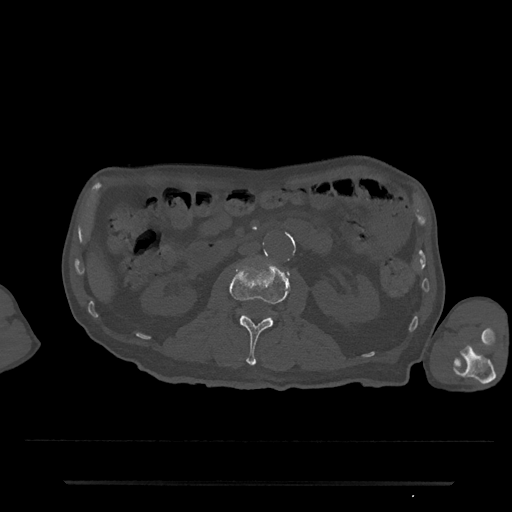
CT including the spine, one axial slice. Slice 42 of 797 in the series (ordered by position). 120 kVp. Bone window (W 1800 / L 400 HU). 0.5 mm slice thickness. 512 × 512 image matrix, field of view 427 × 427 mm. Patient: male, 74 years. Case-level facts recorded for this patient, not image findings: primary cancer: prostate.
Annotated regions visible in this slice (semi-automatic segmentation, software-assisted and operator-edited):
- L2 vertebra: bounding box (x1, y1, x2, y2) in pixels: (229, 259, 290, 366)